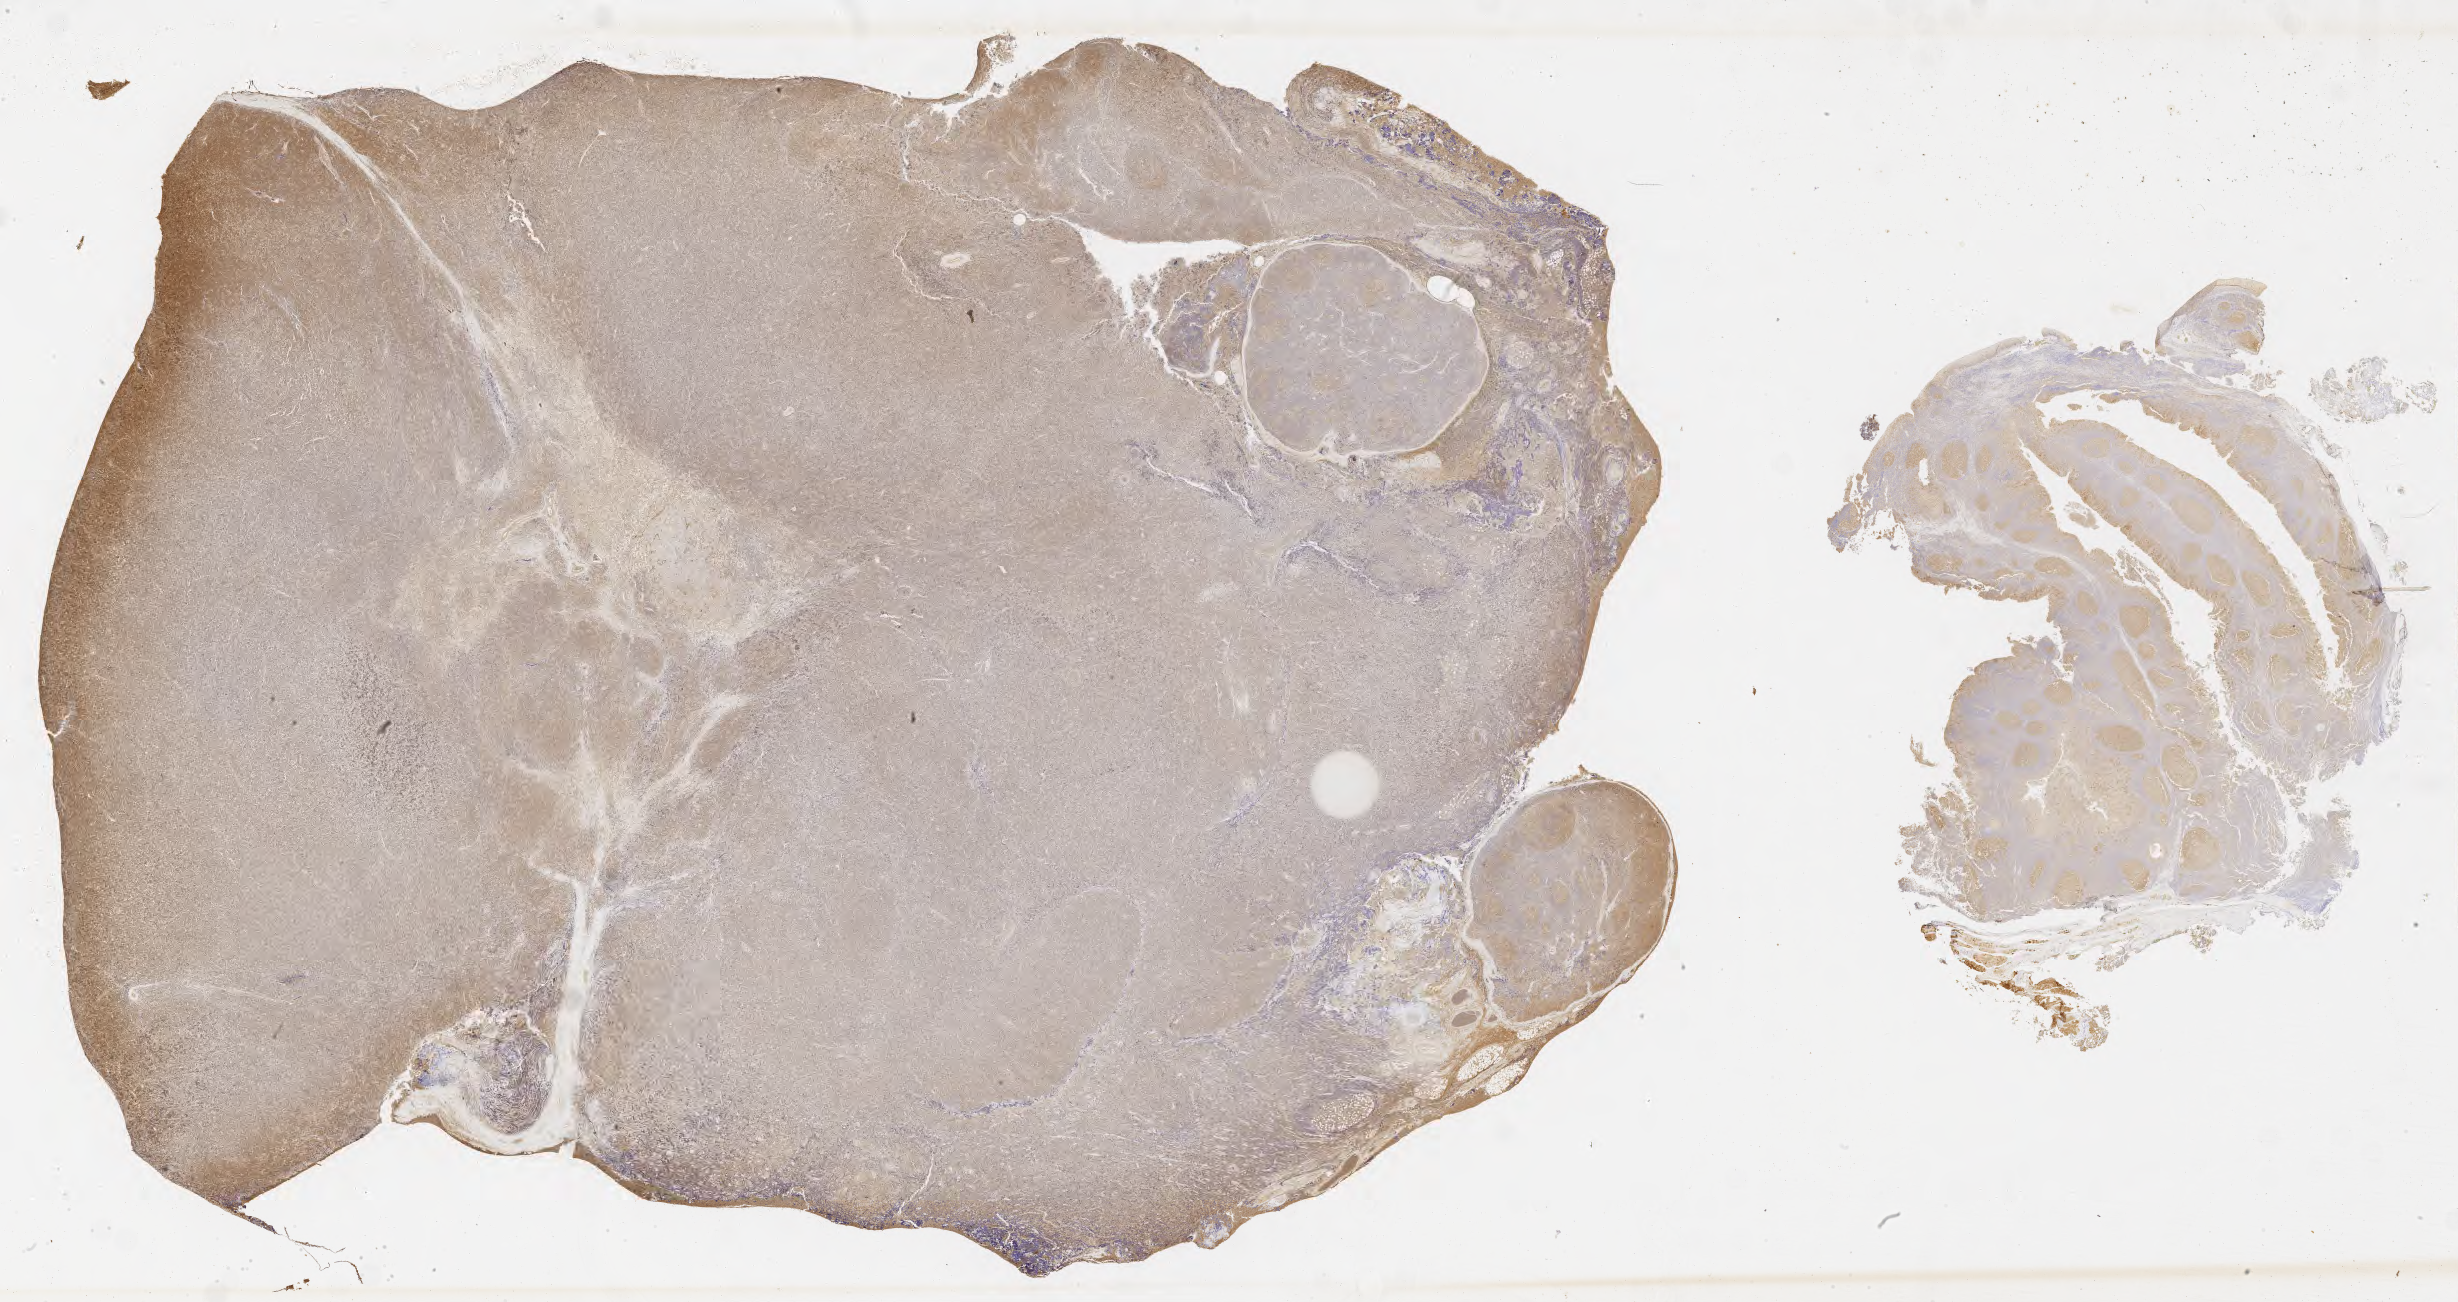
Immunohistochemistry (IHC) whole-slide image stained for BCL6 — shown as a low-resolution overview of the whole scanned area (about 39.8 x 21.1 mm), tumor tissue, site: lymph node of head and neck. Patient: male, age at initial diagnosis 3 years.
Histologic diagnosis: Burkitt lymphoma, NOS.